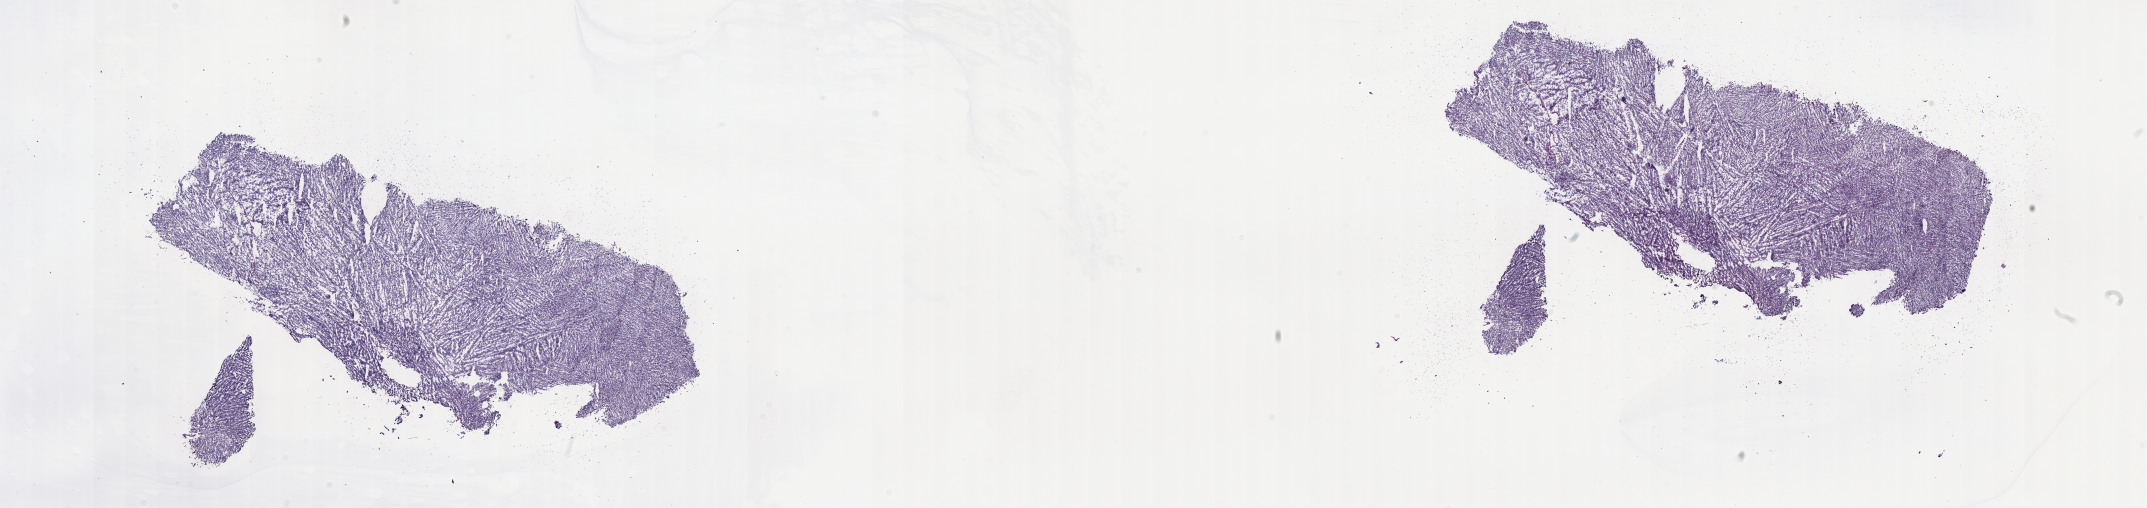
Whole-slide histology image, H&E-stained — low-resolution overview of the scanned area, about 34.7 x 8.2 mm (from a 40x scan), frozen section from the top of the tissue portion, primary tumour sample from the kidney. Female, age 40 years at initial diagnosis. Slide review estimates, as recorded: tumour cells 100%, tumour nuclei 95%.
Histologic diagnosis: Synovial sarcoma, spindle cell.